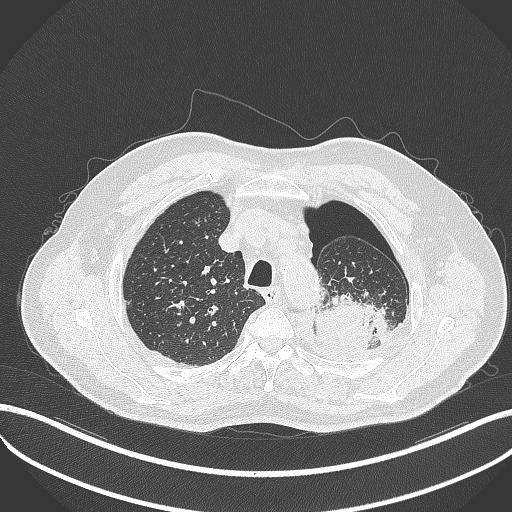
Chest CT, one axial slice; position 403 of 464 along the scan axis; reconstruction kernel B70f; 120 kVp; lung window (W 1500 / L -600 HU); 1 mm slice thickness; 512 × 512 image matrix, field of view 400 × 400 mm. Patient: male, 76 years. Case-level facts recorded for this patient, not image findings: clinical TNM (as recorded): T3 N0 M1b.
Annotated regions visible in this slice (bounding box drawn by a radiologist):
- lung tumour (recorded histology: adenocarcinoma): bounding box [x1, y1, x2, y2] px = [312, 293, 390, 353]